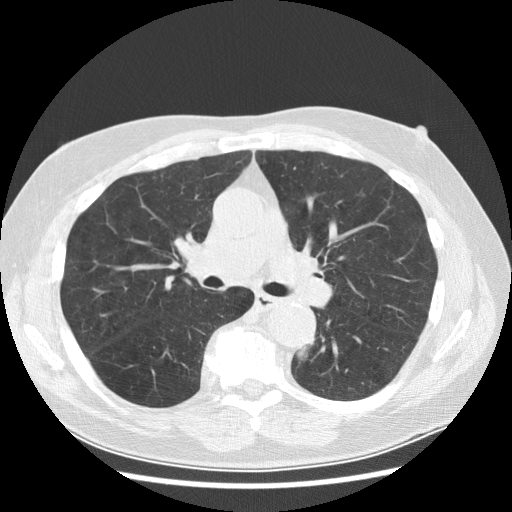
Low-dose screening chest CT, one axial slice. Position 171 of 282 along the scan axis. Lung window (W 1500 / L -600 HU). 2.5 mm slice thickness. 512 × 512 image matrix, field of view 370 × 370 mm.
Structures marked on this image (outlined manually by an expert reader):
- lesion 1 (tumor, lower lobe of left lung): box from (x=296, y=346) to (x=308, y=360) px